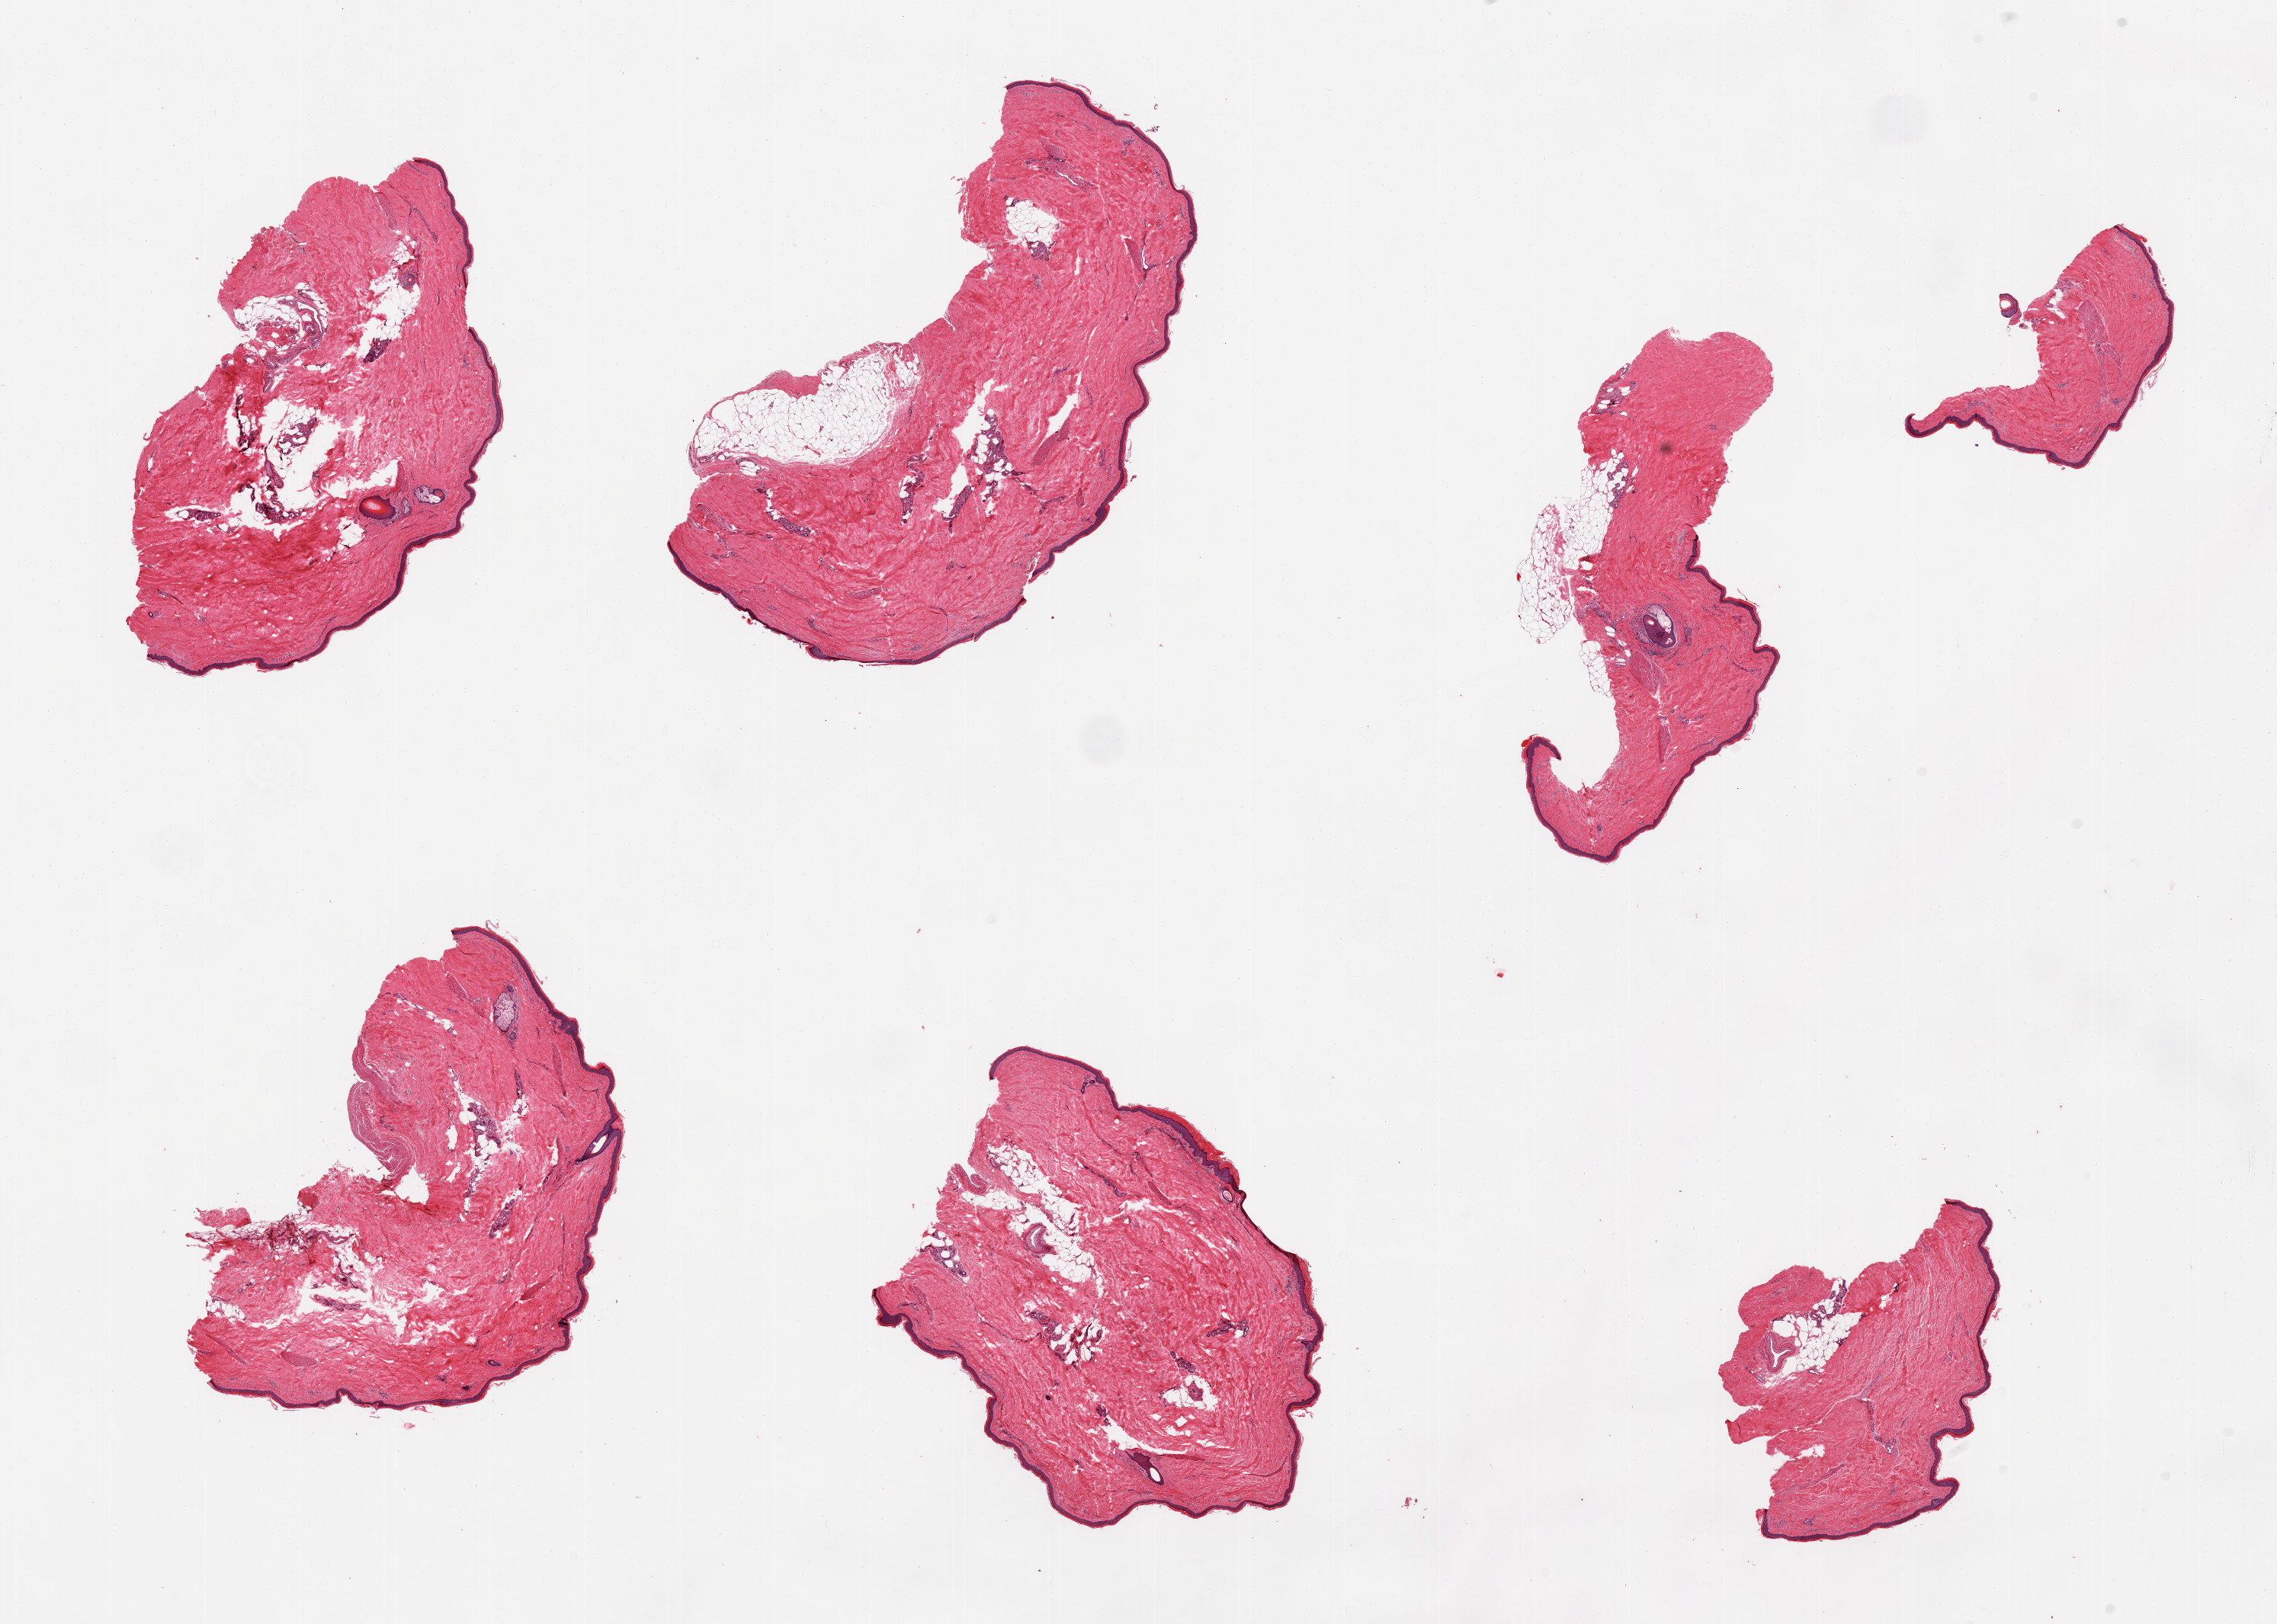
H&E whole-slide image, shown as a low-resolution overview of the whole scanned area (about 23.6 x 16.9 mm, from a 20x scan). PAXgene-fixed, paraffin-embedded tissue. Sampled site (target tissue): skin of lower leg. Tissue donor sample. Male donor.
Pathologist's review note for this sample: 6 pieces, minimal dermal fat; squamous epithelium is ~50 microns.